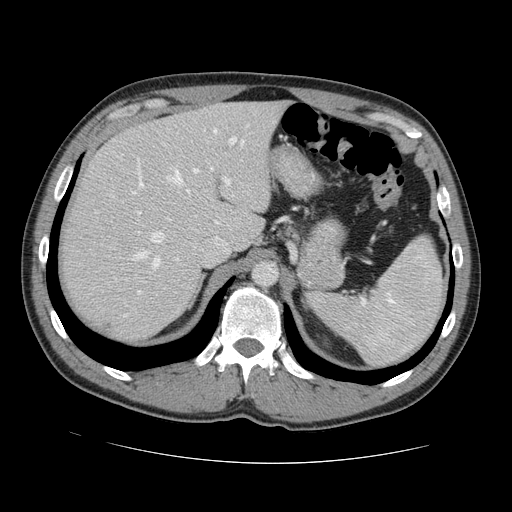
Contrast-enhanced abdominal CT, one axial slice. Position 97 of 131 along the scan axis. 120 kVp. Intravenous contrast given. Soft-tissue window (W 400 / L 40 HU). 2.5 mm slice thickness. 512 × 512 image matrix, field of view 380 × 380 mm. Male patient, age 40 years. From the clinical record (not read from this slice): diagnosis: colorectal cancer liver metastases, imaged before liver resection; multiple liver metastases: yes; largest metastasis: 2.9 cm; disease in both lobes: yes.
Structures marked on this image (outlined manually by an expert reader):
- hepatic veins: bounding box [x1, y1, x2, y2] px = [123, 141, 244, 317]
- liver: [63, 102, 283, 341]
- planned liver remnant (the part of the liver to remain after resection): [98, 102, 284, 248]
- portal vein (with intrahepatic branches): [132, 137, 237, 294]
- liver metastasis: [105, 324, 112, 332]